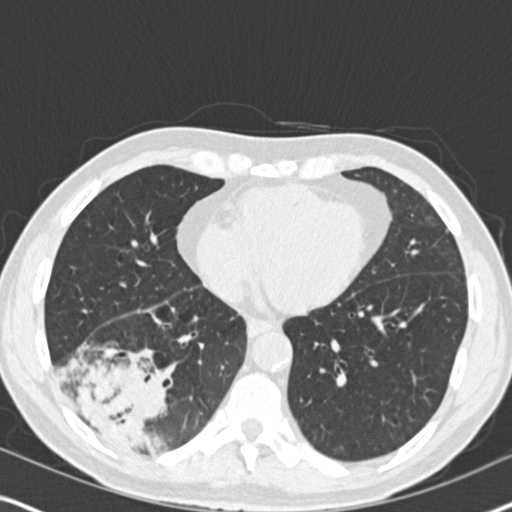
Axial slice from a low-dose chest CT screening exam, second screening round (one year after baseline), lung window (W 1500 / L -600 HU), 2 mm slice thickness, slice 109 of 182 in the series. Male participant, aged 61 years at enrolment. Current smoker at enrolment.
Expert reader's lesion annotation, bounding box [x1, y1, x2, y2] px = [49, 324, 189, 464]. Screening reader's record for this exam (one nodule recorded; not confirmed to be the boxed lesion): non-calcified nodule or mass ≥4 mm, right lower lobe, 90 × 80 mm, soft tissue attenuation, pre-existing on the prior screen: yes; interval growth: yes.